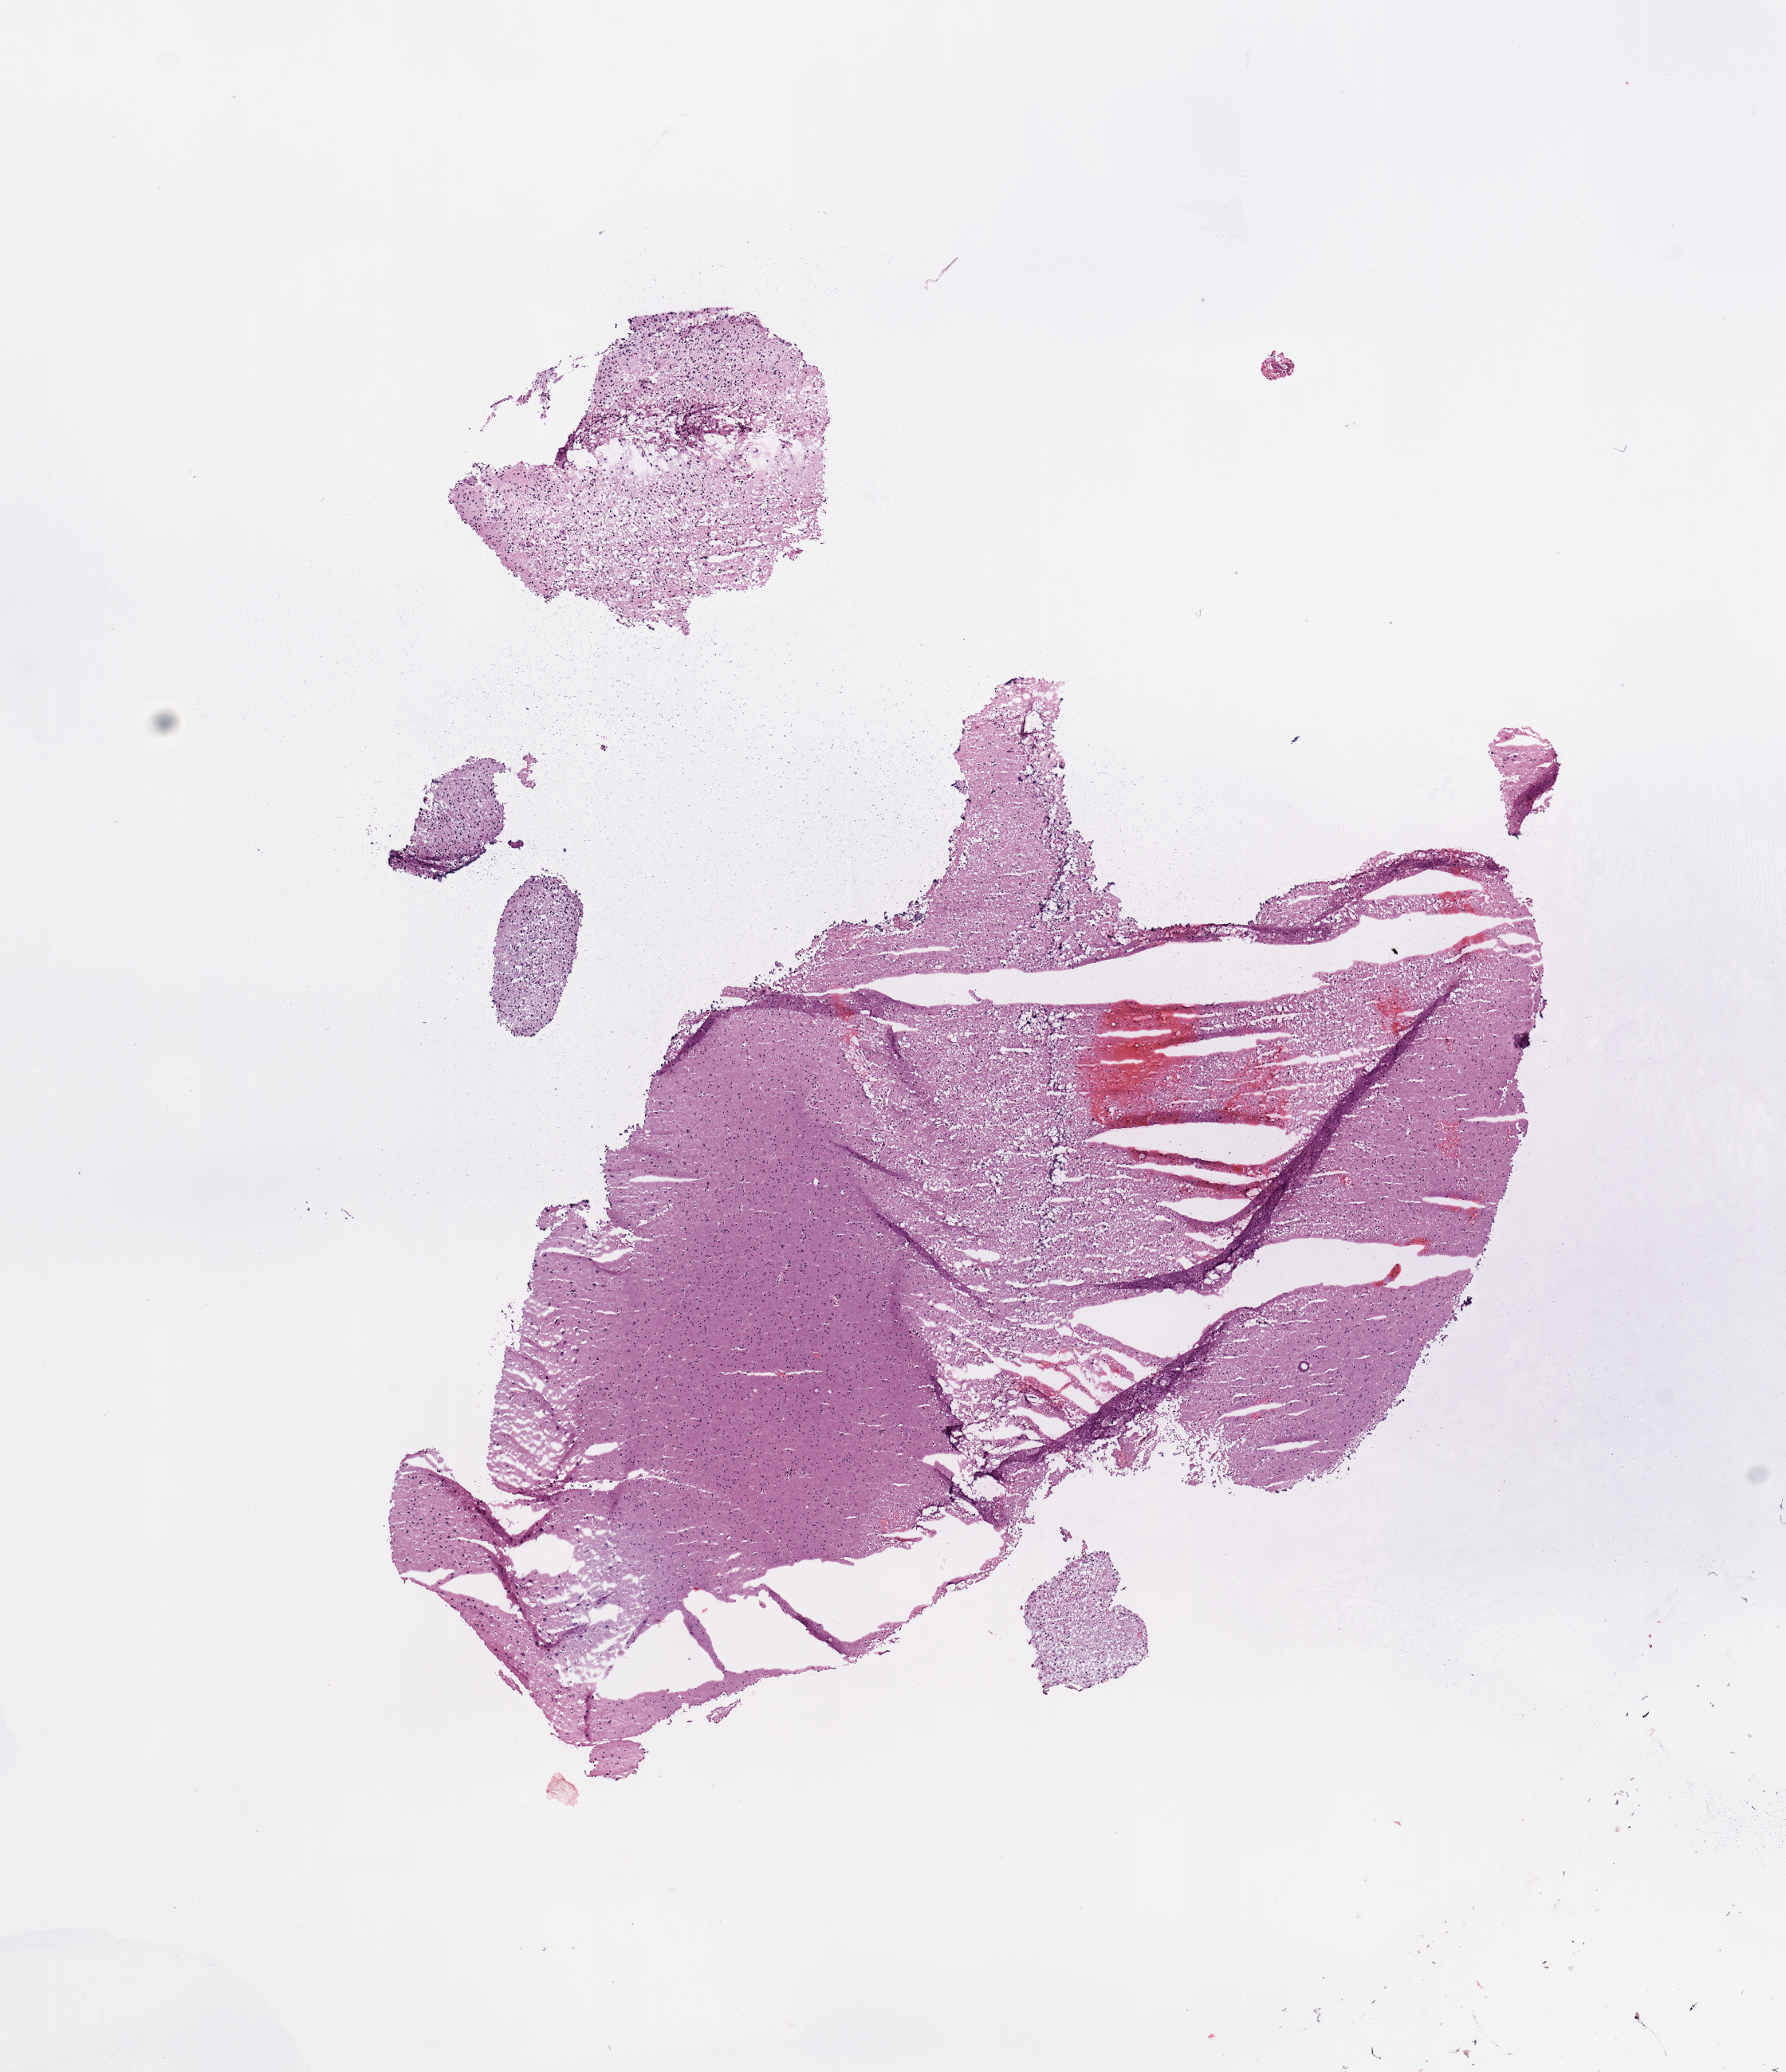
H&E whole-slide image, a low-resolution overview of the entire scanned area, about 8.9 x 10.3 mm; brain, tumour tissue. Male, 61 y/o.
• primary tumour site (as recorded): temporal lobe
• patient diagnosis (cohort enrolment): glioblastoma multiforme (brain)